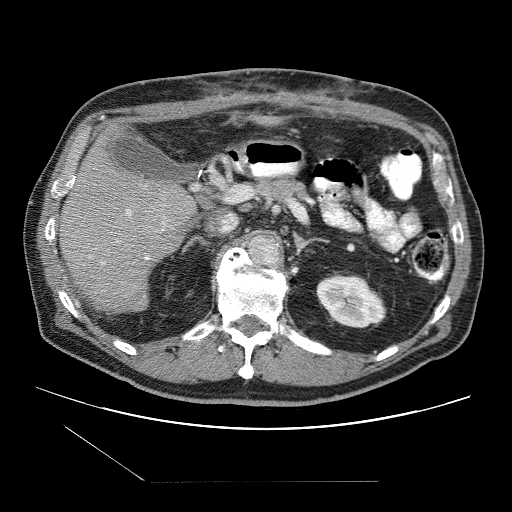
Contrast-enhanced abdominal CT (liver protocol), one axial slice. Slice 50 of 109 in the series (ordered by position). One of 2 acquisitions stored at this slice position. Soft-tissue window (W 400 / L 40 HU). 512 × 512 image matrix, field of view 400 × 400 mm. From the clinical record (not read from this slice): diagnosis: hepatocellular carcinoma (patient treated with transarterial chemoembolisation; whether this scan precedes or follows treatment is not stated here); TNM stage (as recorded): Stage-IIIB; Child-Pugh class: A; tumour differentiation: well differentiated; tumour nodularity: multinodular.
Structures marked on this image (semi-automatically segmented with operator editing):
- liver parenchyma outside the tumour (the mass and vessels are separate outlines, so this box may not span the whole liver): box from (x=58, y=123) to (x=196, y=310) px
- liver vessels: (x=102, y=209)–(x=166, y=264)